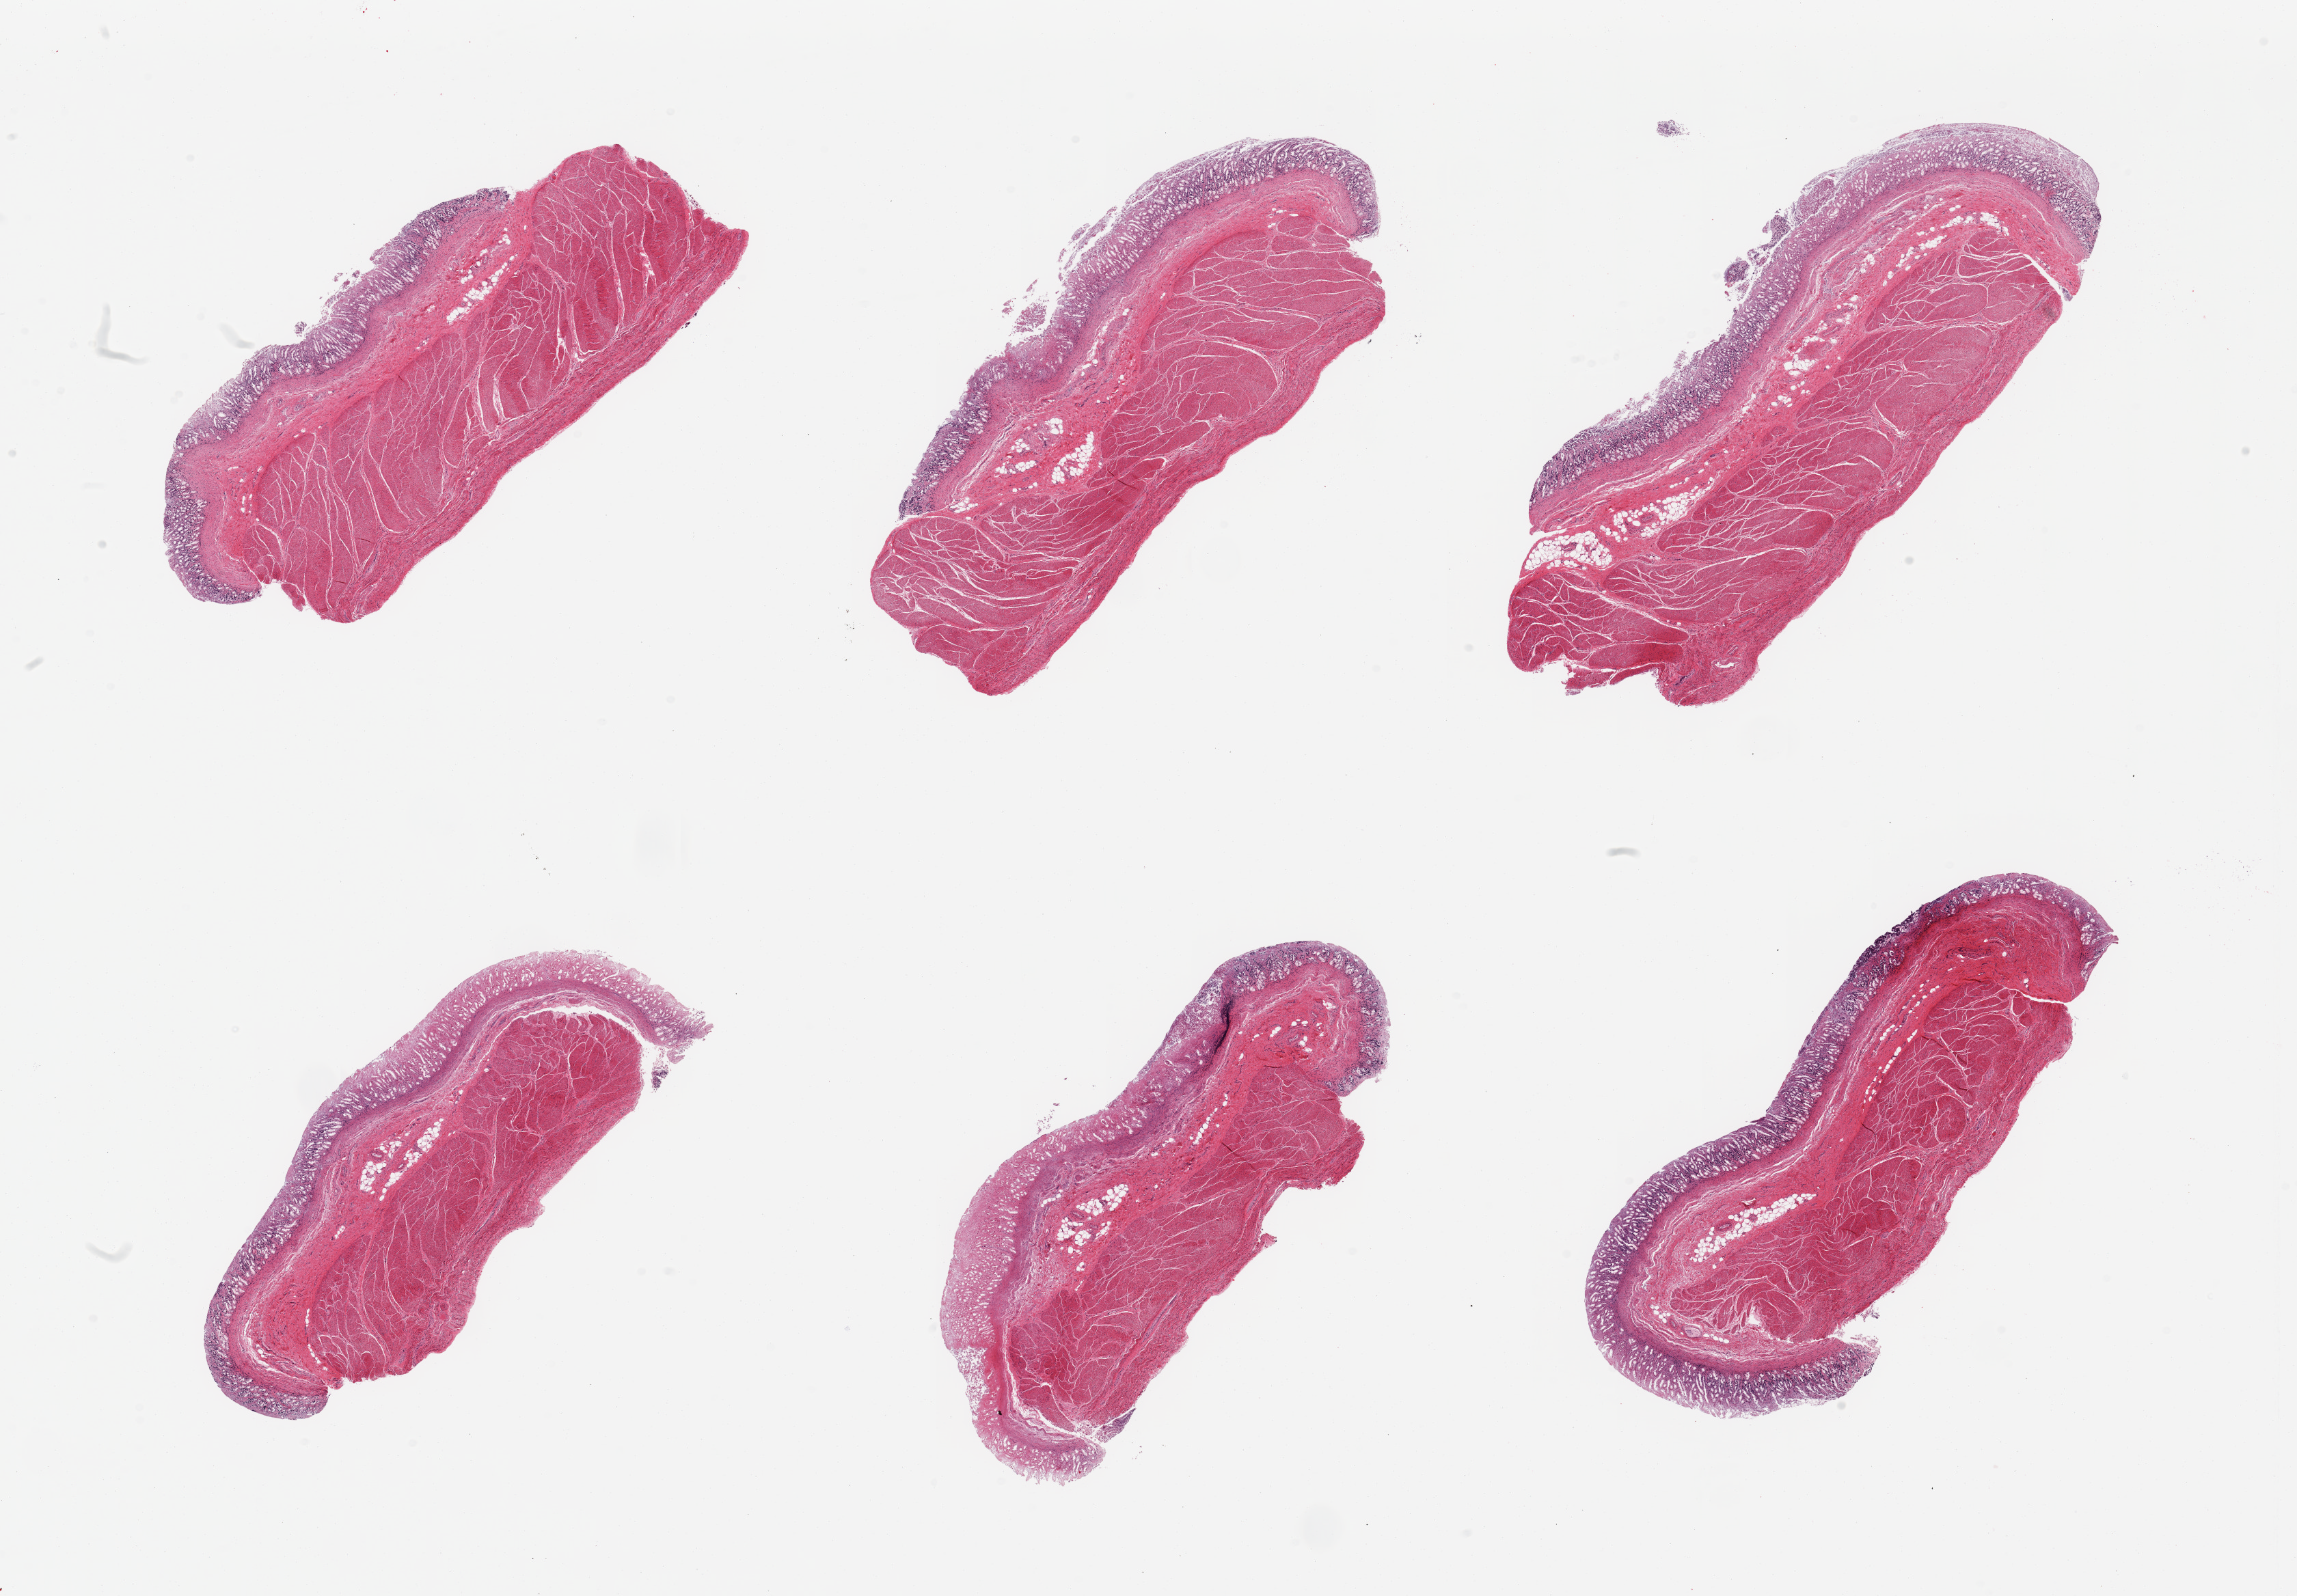
Digitized haematoxylin and eosin-stained section — a low-resolution overview of the entire scanned area, about 26.6 x 18.5 mm. PAXgene-fixed, paraffin-embedded tissue. Sampled site (target tissue): stomach. Tissue donor sample. Female donor.
Reviewer comment on this tissue sample: 6 pieces; full thickness sections, mucosa (3), muscularis (2).